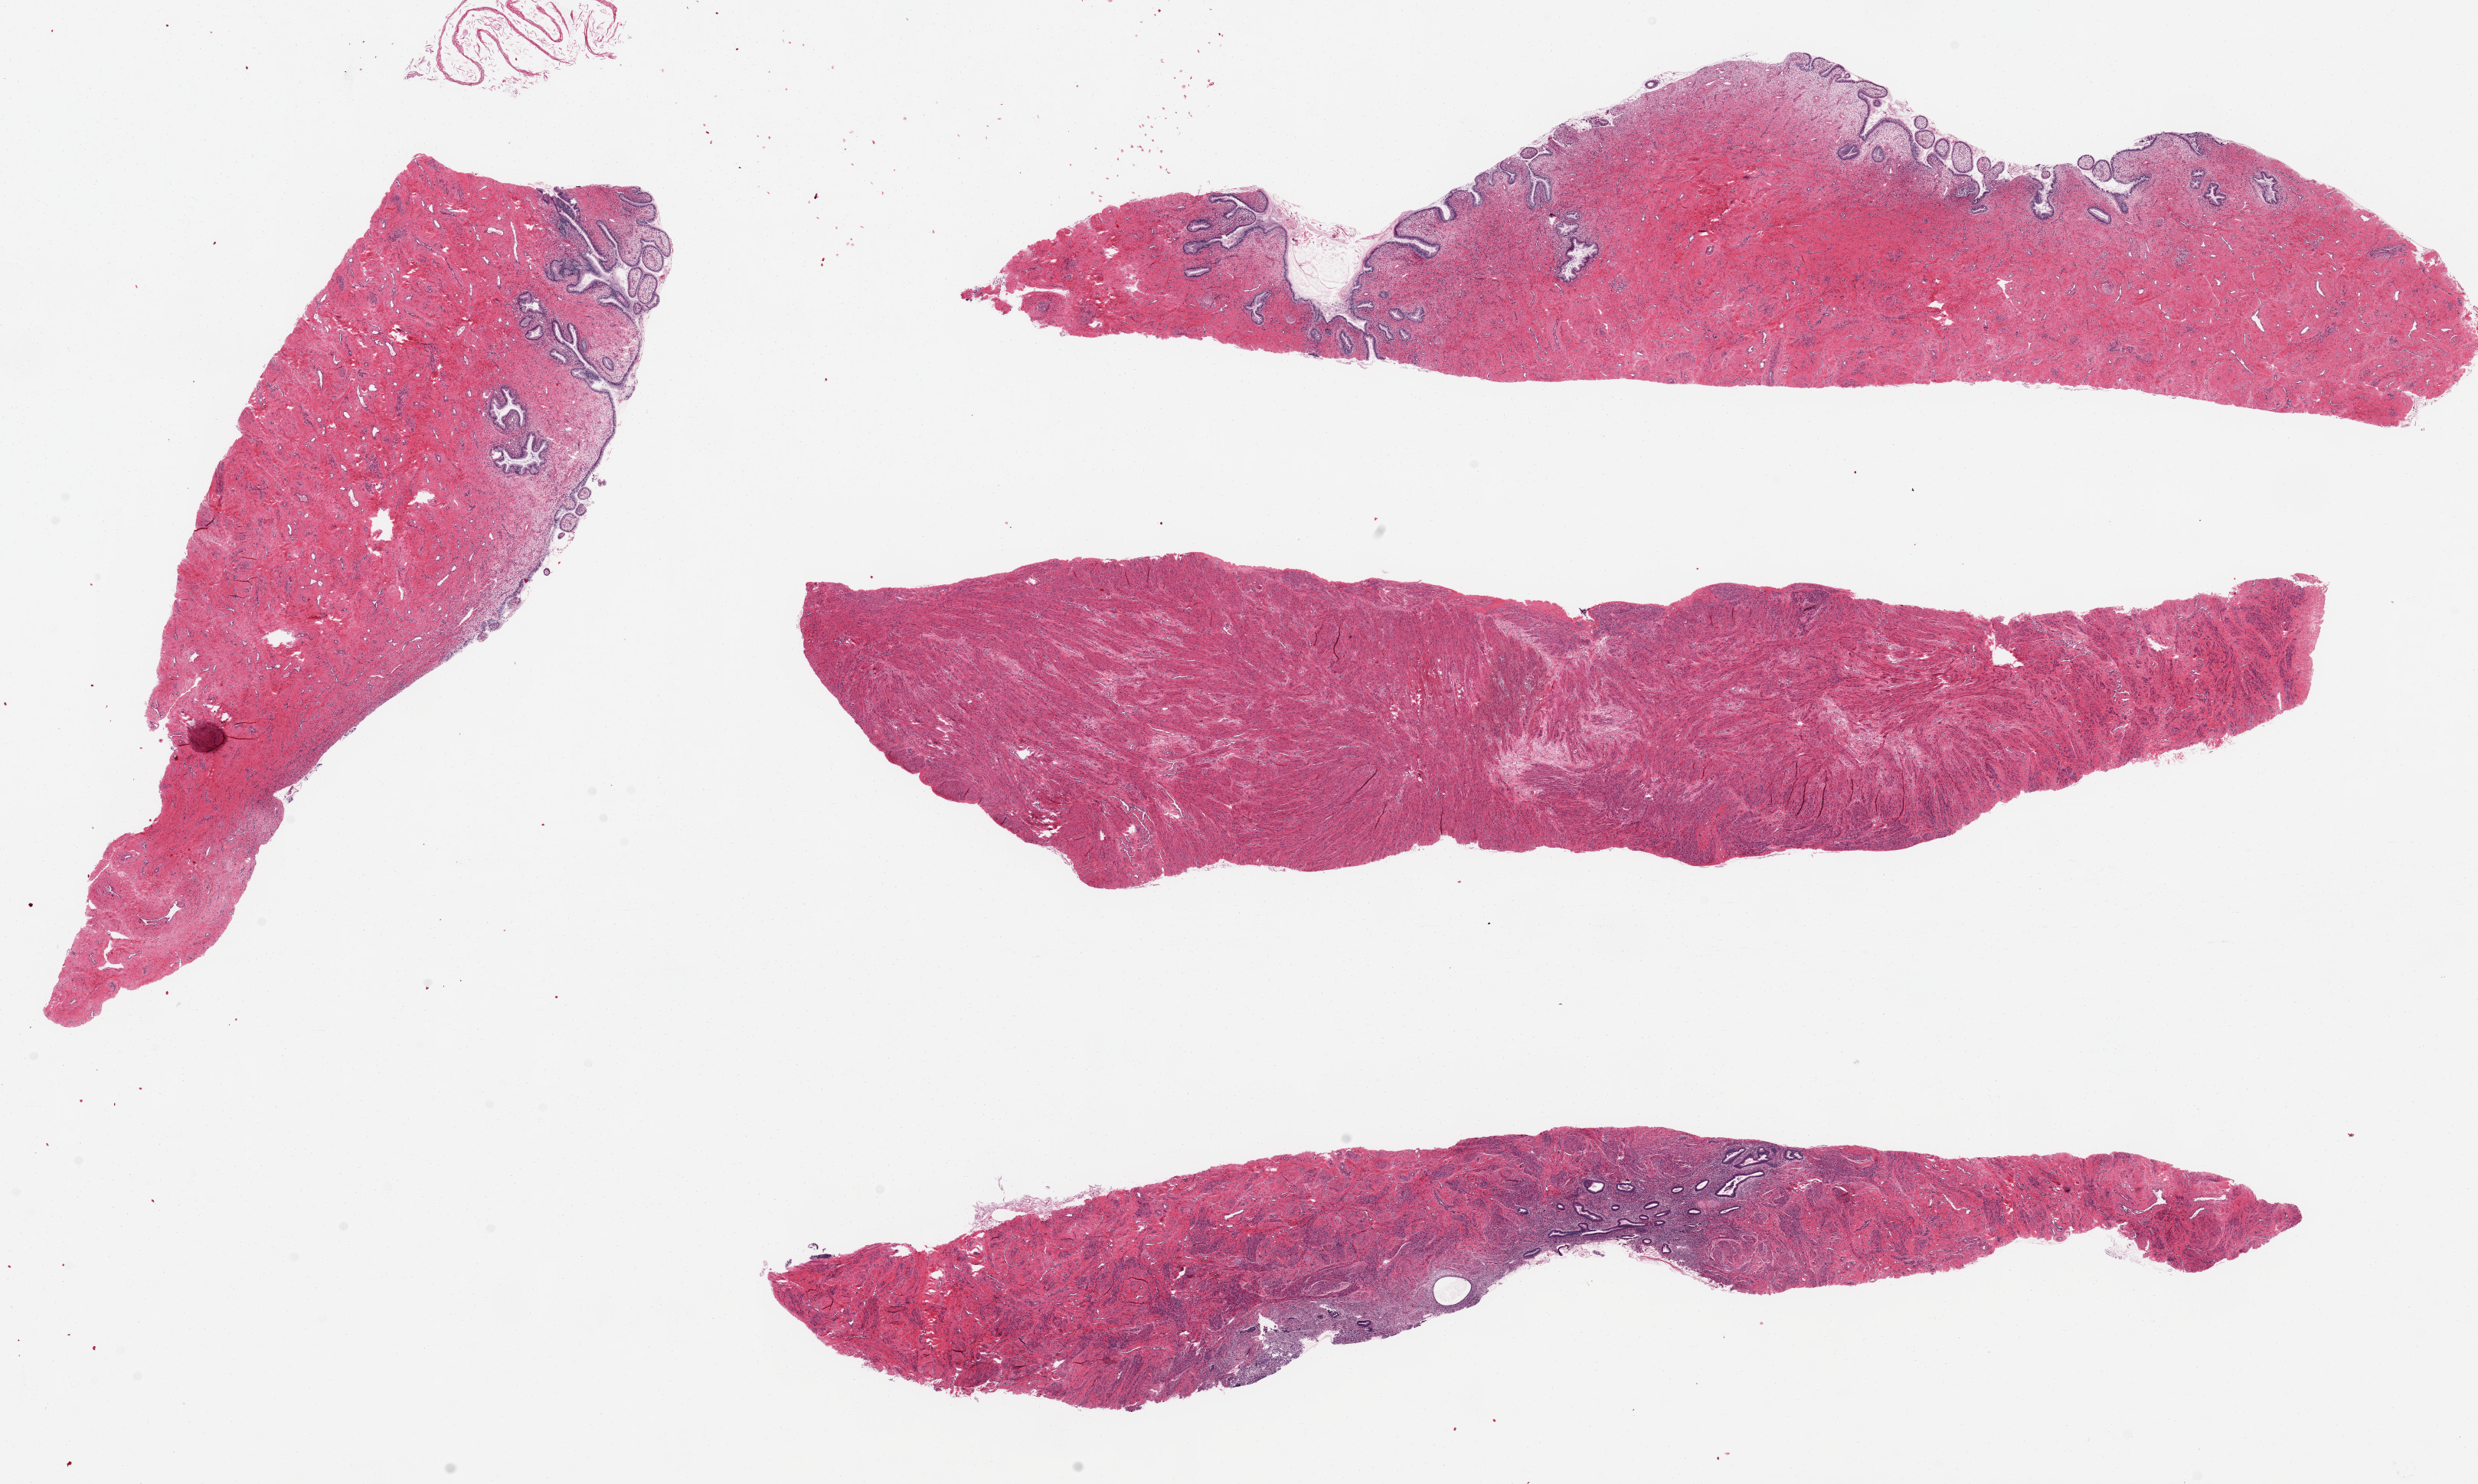
Hematoxylin and eosin (H&E) whole-slide image — a low-resolution overview of the entire scanned area, about 25.6 x 15.3 mm; PAXgene-fixed, paraffin-embedded tissue; section of endocervix (target tissue); donor tissue sample. Donor sex: female.
Review note (as recorded): 4 pieces up to 15x3.4 mm 2 with endocervix, 1 with endometrium, 1 without epithelium.